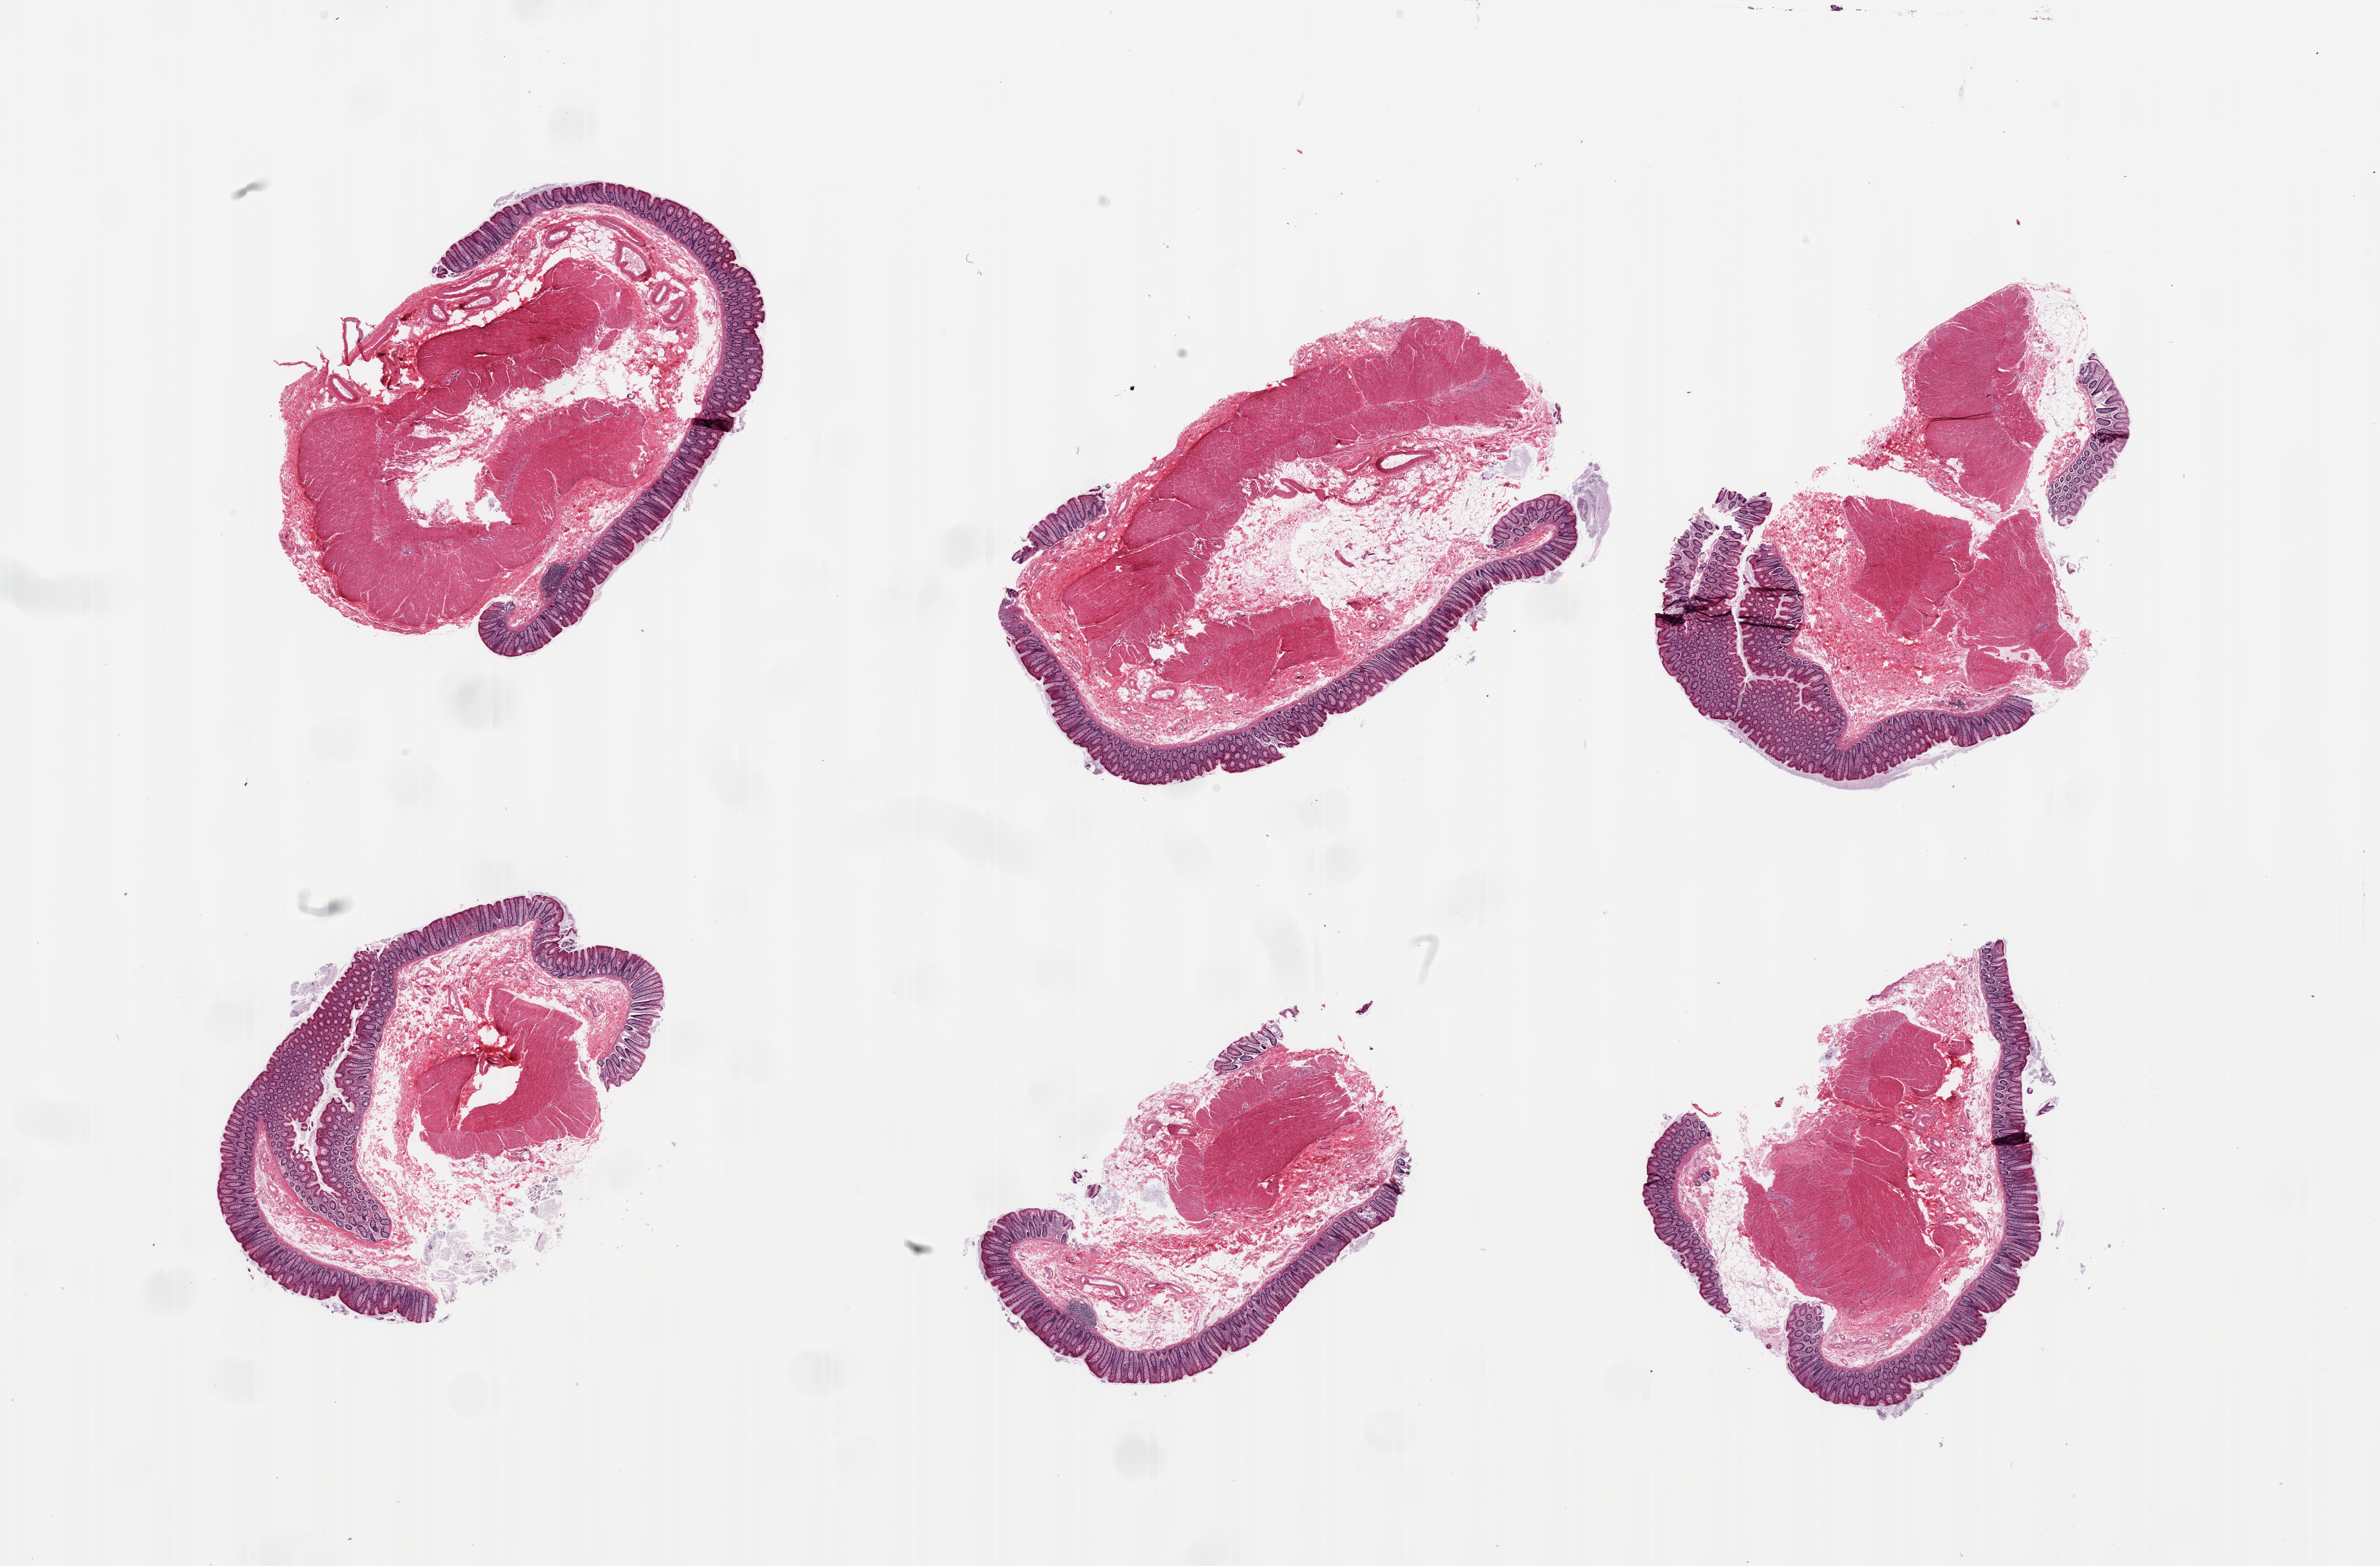
Hematoxylin and eosin (H&E) whole-slide image, low-resolution overview of the scanned area, about 28.5 x 18.8 mm, PAXgene-fixed paraffin-embedded (PFPE) section, target tissue: transverse colon, donor tissue sample. Male donor.
Review note (as recorded): 6 pieces; all contain mucosa and muscle.